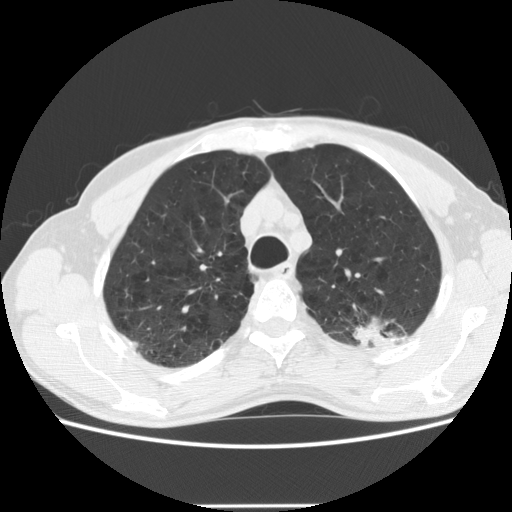
Chest CT (low-dose screening protocol), one axial image. Baseline screening round. Lung window (W 1500 / L -600 HU). Standard (soft-tissue) reconstruction kernel (STANDARD). Slice 40 of 191 in the series. 512 × 512 image matrix, field of view 352 × 352 mm. Male participant, aged 64 years at enrolment.
Lesion marked by an expert reader, bounding box (x1, y1, x2, y2) in pixels: (341, 289, 427, 359). Reader record for this screening exam (exam-level; its link to the box is not recorded): non-calcified nodule or mass ≥4 mm, left upper lobe, 27 × 19 mm, poorly defined margins, soft tissue attenuation. Official screen result: positive, change unspecified: nodule(s) >= 4 mm or enlarging nodule(s), mass(es), or other non-specific abnormalities suspicious for lung cancer. Lung cancer was diagnosed 23 days after this screen: adenocarcinoma, NOS, left upper lobe, moderately differentiated (G2), stage IA (AJCC 6th edition), 29 mm at pathology.